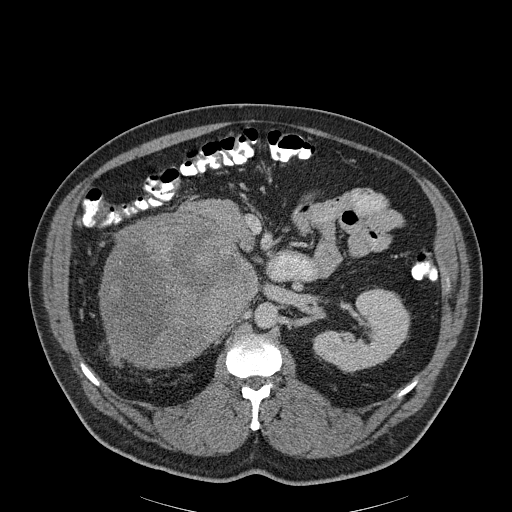
Contrast-enhanced abdominal CT, one axial slice. Slice 119 of 186 in the series (ordered by position). Reconstruction kernel B30f. 120 kVp. Soft-tissue window (W 400 / L 40 HU). 3 mm slice thickness. 512 × 512 image matrix, field of view 464 × 464 mm. Patient: male, 56 years. Case-level facts recorded for this patient, not image findings: diagnosis: adrenocortical carcinoma; tumour side: right adrenal; tumour size at pathology: 18 cm; Ki-67 index: 2 %; stage (as recorded): 3.
Annotated regions visible in this slice (semi-automatically segmented with operator editing):
- mass: bounding box (x1, y1, x2, y2) in pixels: (102, 215, 245, 365)